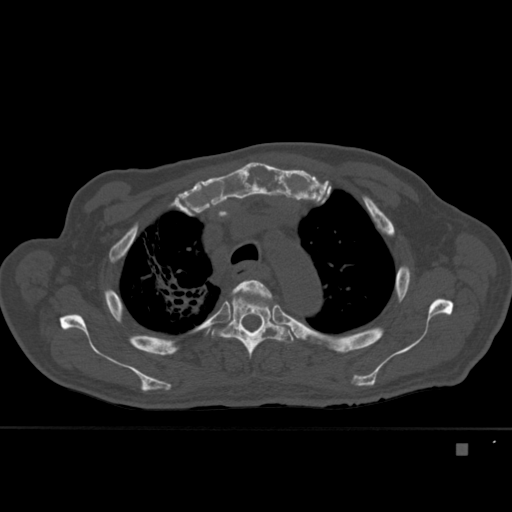
CT including the spine, one axial slice. Bone window (W 1800 / L 400 HU). 512 × 512 image matrix, field of view 378 × 378 mm. Patient: male, 75 years. Case-level facts recorded for this patient, not image findings: primary cancer: prostate.
Annotated regions visible in this slice (semi-automatic segmentation, software-assisted and operator-edited):
- T3 vertebra: box from (x=231, y=280) to (x=272, y=301) px
- T4 vertebra: (x=211, y=295)–(x=294, y=359)